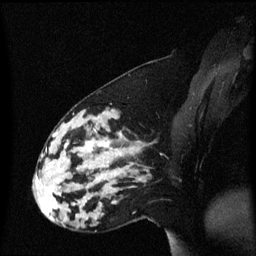
Breast MRI (dynamic contrast-enhanced), one sagittal slice. Slice 21 of 60 in the series (ordered by position). Dynamic contrast-enhanced series, image 2 of 3 at this slice position (ordered by acquisition). 1.5 T. TE 4.2 ms, TR 8.4 ms. 2 mm slice thickness. 256 × 256 image matrix, field of view 210 × 210 mm. Female patient, age 33 years. Case-level facts recorded for this patient, not image findings: setting: breast cancer imaged before/during neoadjuvant chemotherapy; receptor status: triple-negative.
Structures marked on this image (semi-automatic segmentation, software-assisted and operator-edited):
- analysis volume of interest (the breast-tissue region the enhancement analysis was run in; not a lesion): bounding box (x1, y1, x2, y2) in pixels: (44, 123, 139, 189)
- tumour enhancement mask (voxels above the 70 % enhancement threshold inside the analysis volume of interest): (48, 142, 124, 170)